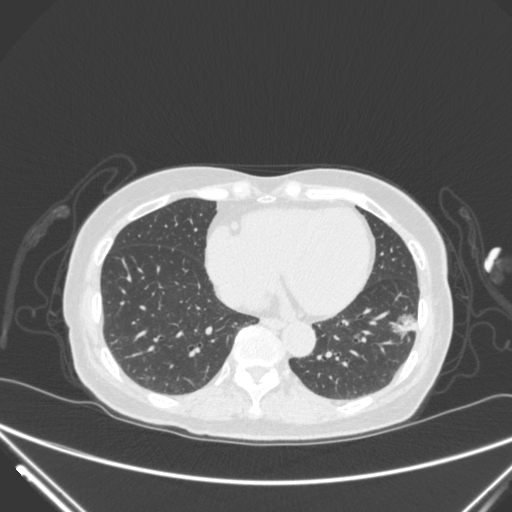
Chest CT, one axial slice; slice 105 of 310 in the series (ordered by position); lung window (W 1500 / L -600 HU); 512 × 512 image matrix. Patient: female, 82 years. From the clinical record (not read from this slice): clinical TNM (as recorded): T1c N0 M0.
Structures marked on this image (bounding box drawn by a radiologist):
- lung tumour (recorded histology: adenocarcinoma): box from (x=384, y=303) to (x=420, y=353) px